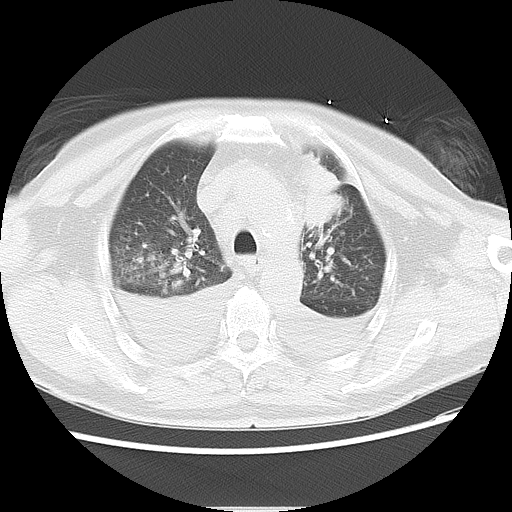
Chest CT, one axial slice; slice 20 of 22 in the series (ordered by position); reconstruction kernel LUNG; lung window (W 1500 / L -600 HU); 512 × 512 image matrix. Patient: male, 66 years. From the clinical record (not read from this slice): clinical TNM (as recorded): T1c N0 M0.
Structures marked on this image (bounding box drawn by a radiologist):
- lung tumour (recorded histology: adenocarcinoma): bounding box (x1, y1, x2, y2) in pixels: (293, 149, 346, 233)